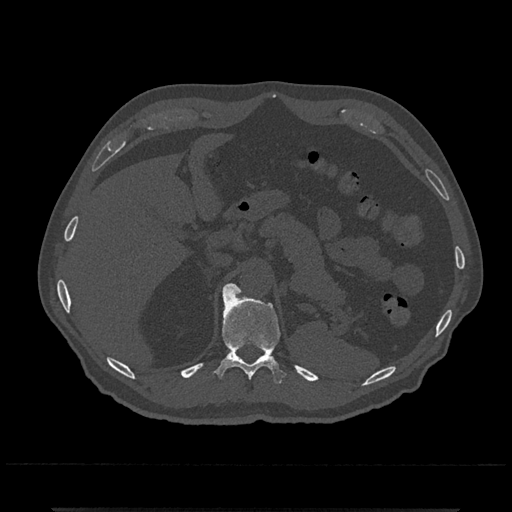
CT including the spine, one axial slice; slice 488 of 797 in the series (ordered by position); 120 kVp; bone window (W 1800 / L 400 HU); 0.5 mm slice thickness; 512 × 512 image matrix, field of view 393 × 393 mm. Male patient, age 67 years. Case-level facts recorded for this patient, not image findings: primary cancer: prostate.
Outlined on this slice (semi-automatically segmented with operator editing):
- T11 vertebra: bounding box <214,284,286,384> (left, top, right, bottom; pixels)
- T12 vertebra: <224,284,241,294>